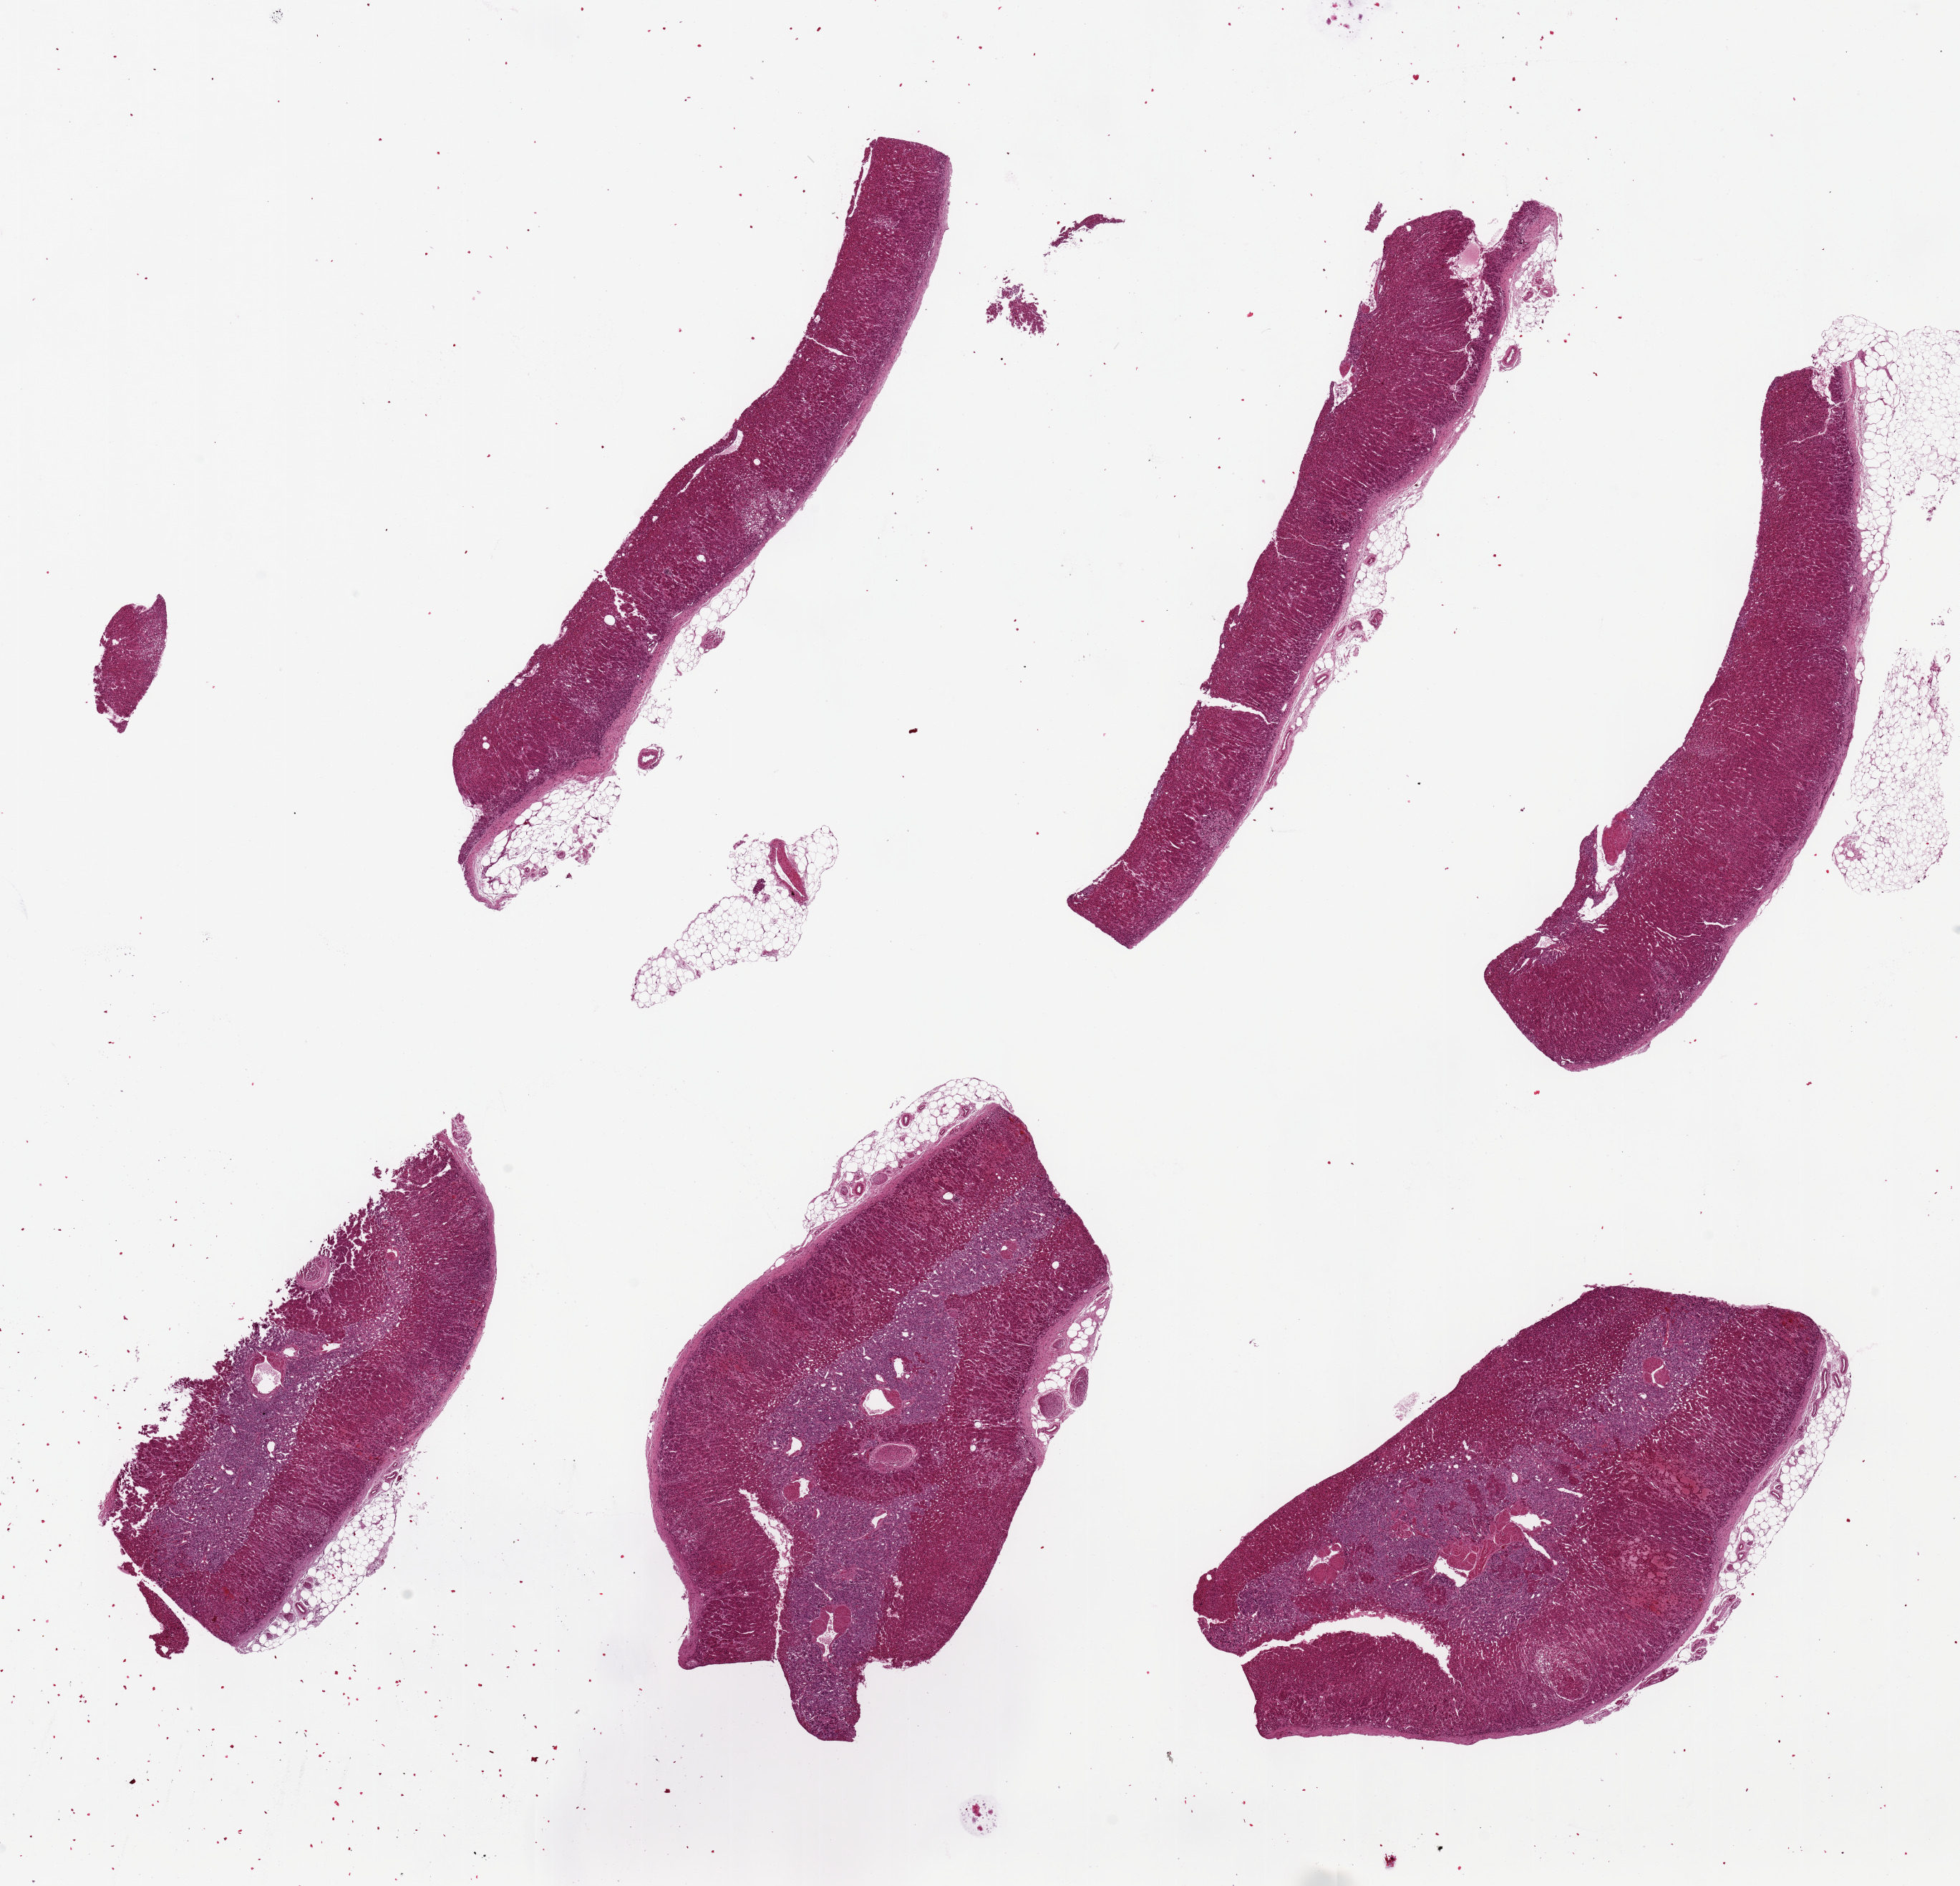
Digitized hematoxylin and eosin (H&E)-stained section, low-resolution overview of the scanned area, about 21.7 x 20.8 mm (from a 20x scan). PAXgene-fixed paraffin-embedded (PFPE) section. Target tissue: adrenal gland. Tissue donor sample. Donor sex: male.
Reviewer comment on this tissue sample: 6 pieces, 3 with ~8x4mm, 3 with cortex can medualla.